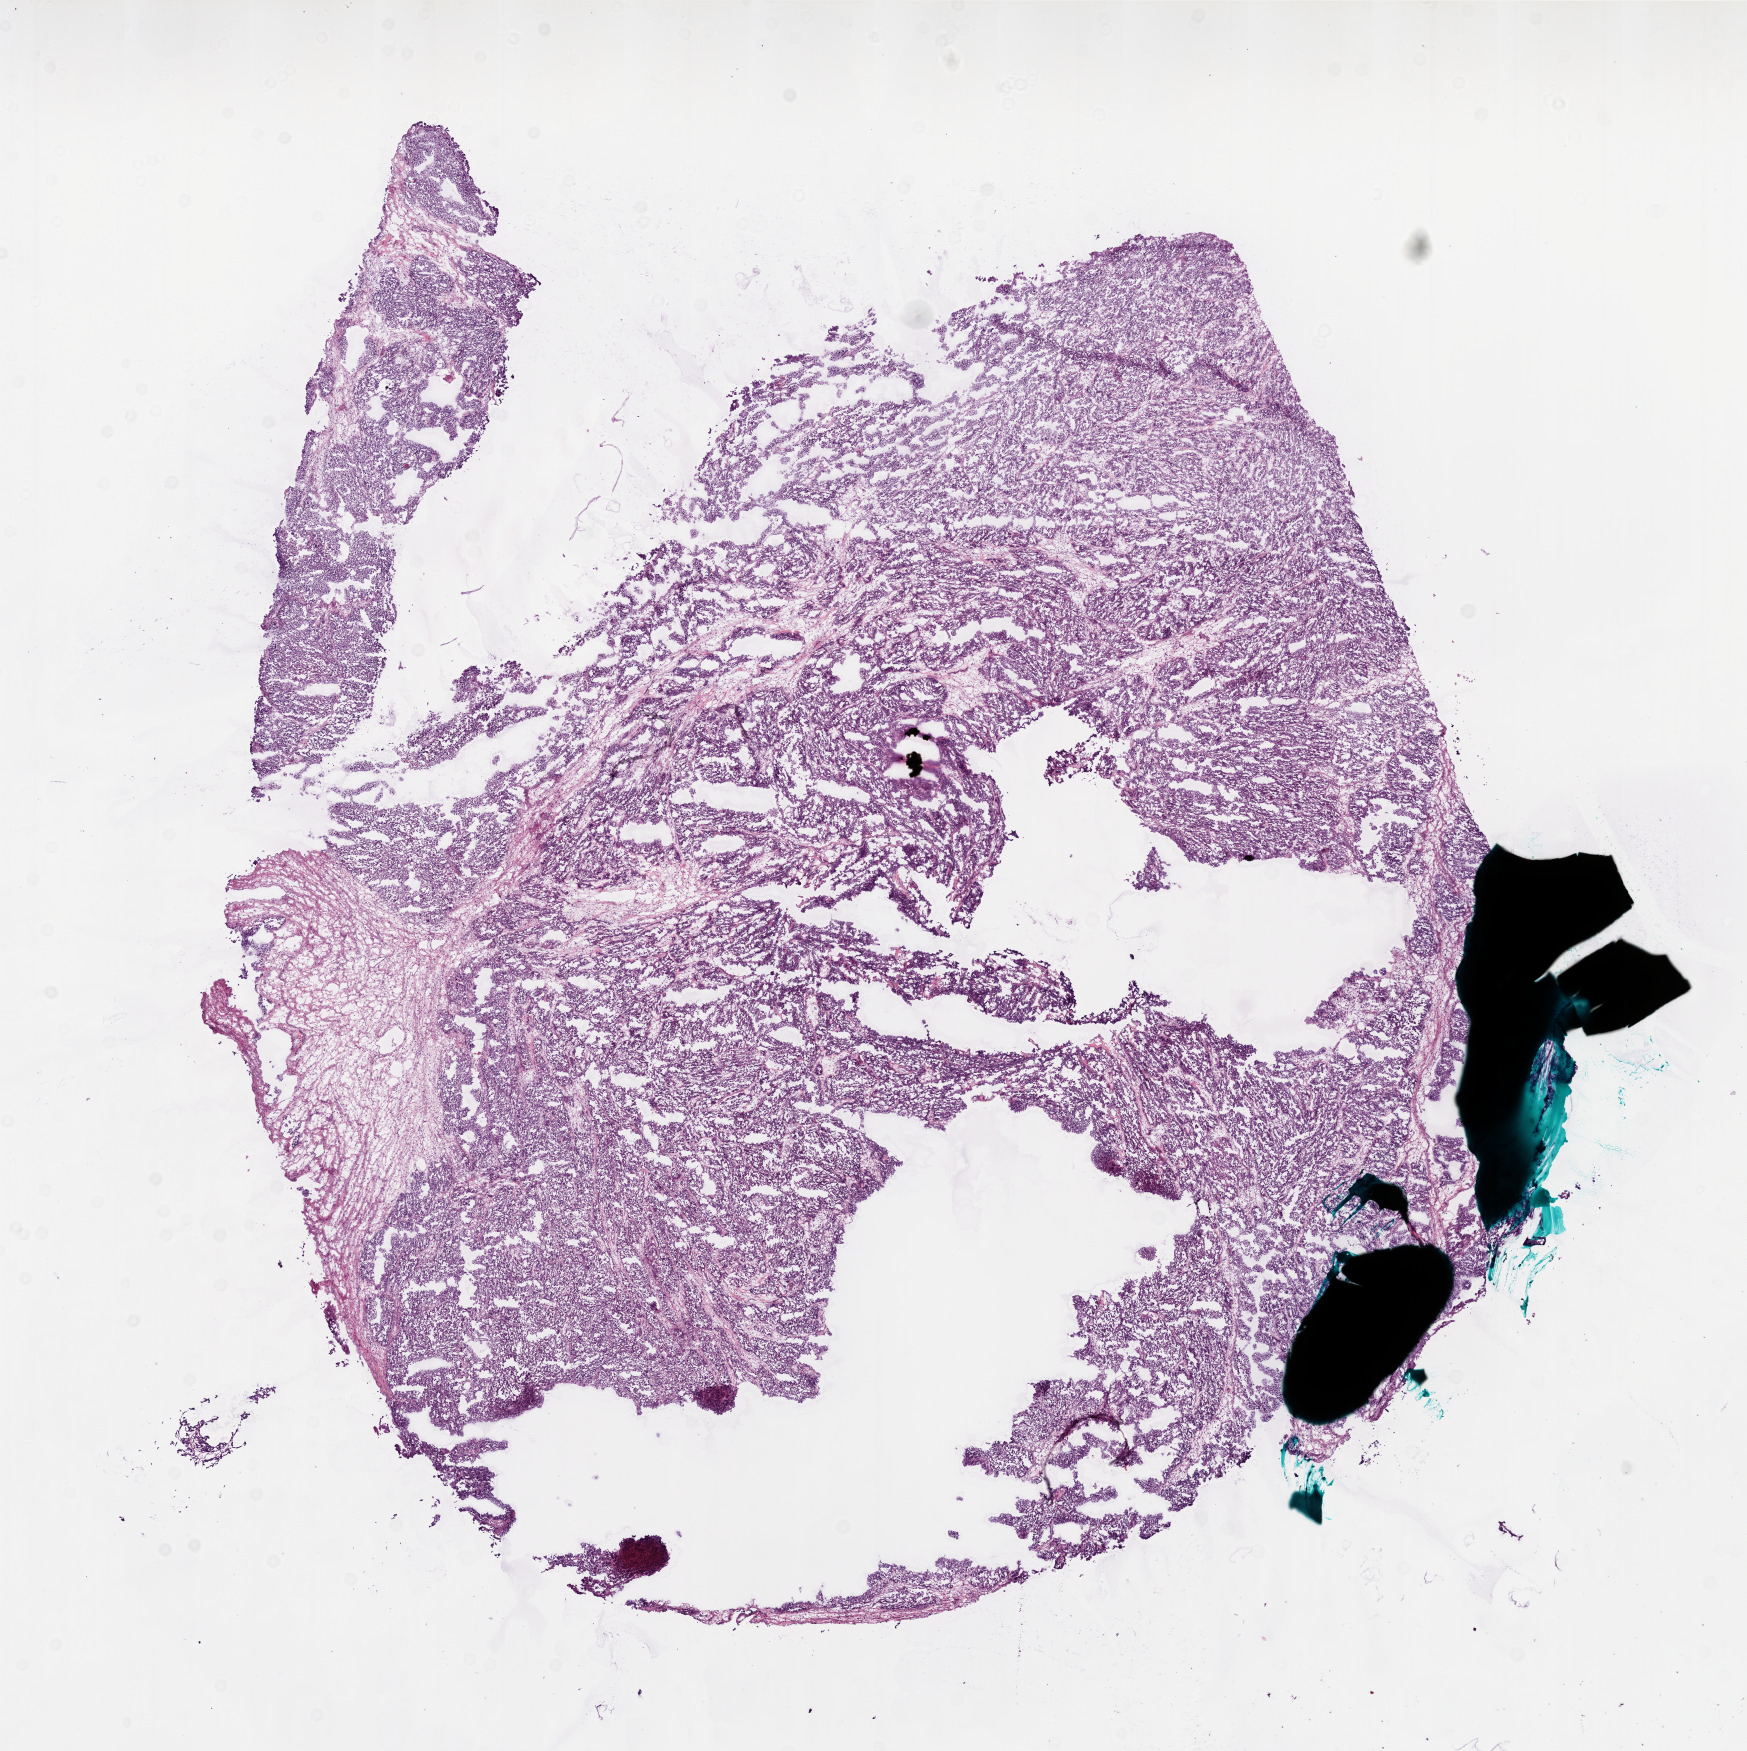
Digitized H&E-stained tissue section (whole slide), a low-resolution overview of the entire scanned area, about 14.0 x 14.0 mm, frozen section from the bottom of the tissue portion, ovary, primary tumour sample. Female patient; age at initial diagnosis 61 years. Histologic grade: G3 (poorly differentiated). Slide review estimates, as recorded: tumour cells 88%, tumour nuclei 90%, normal cells 10%, stromal cells 0%, necrosis 2%.
* FIGO stage: IIIC
* diagnosis: Serous cystadenocarcinoma, NOS